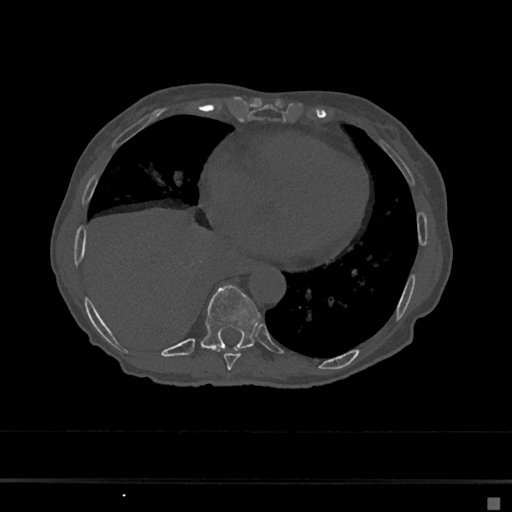
CT including the spine, one axial slice. Position 292 of 797 along the scan axis. Reconstruction kernel Br40s/3. Bone window (W 1800 / L 400 HU). 512 × 512 image matrix, field of view 360 × 360 mm. Female patient, age 68 years. Case-level facts recorded for this patient, not image findings: primary cancer: renal.
Annotated regions visible in this slice (semi-automatically segmented with operator editing):
- T8 vertebra: box from (x=224, y=353) to (x=241, y=370) px
- T9 vertebra: (x=201, y=285)–(x=260, y=351)